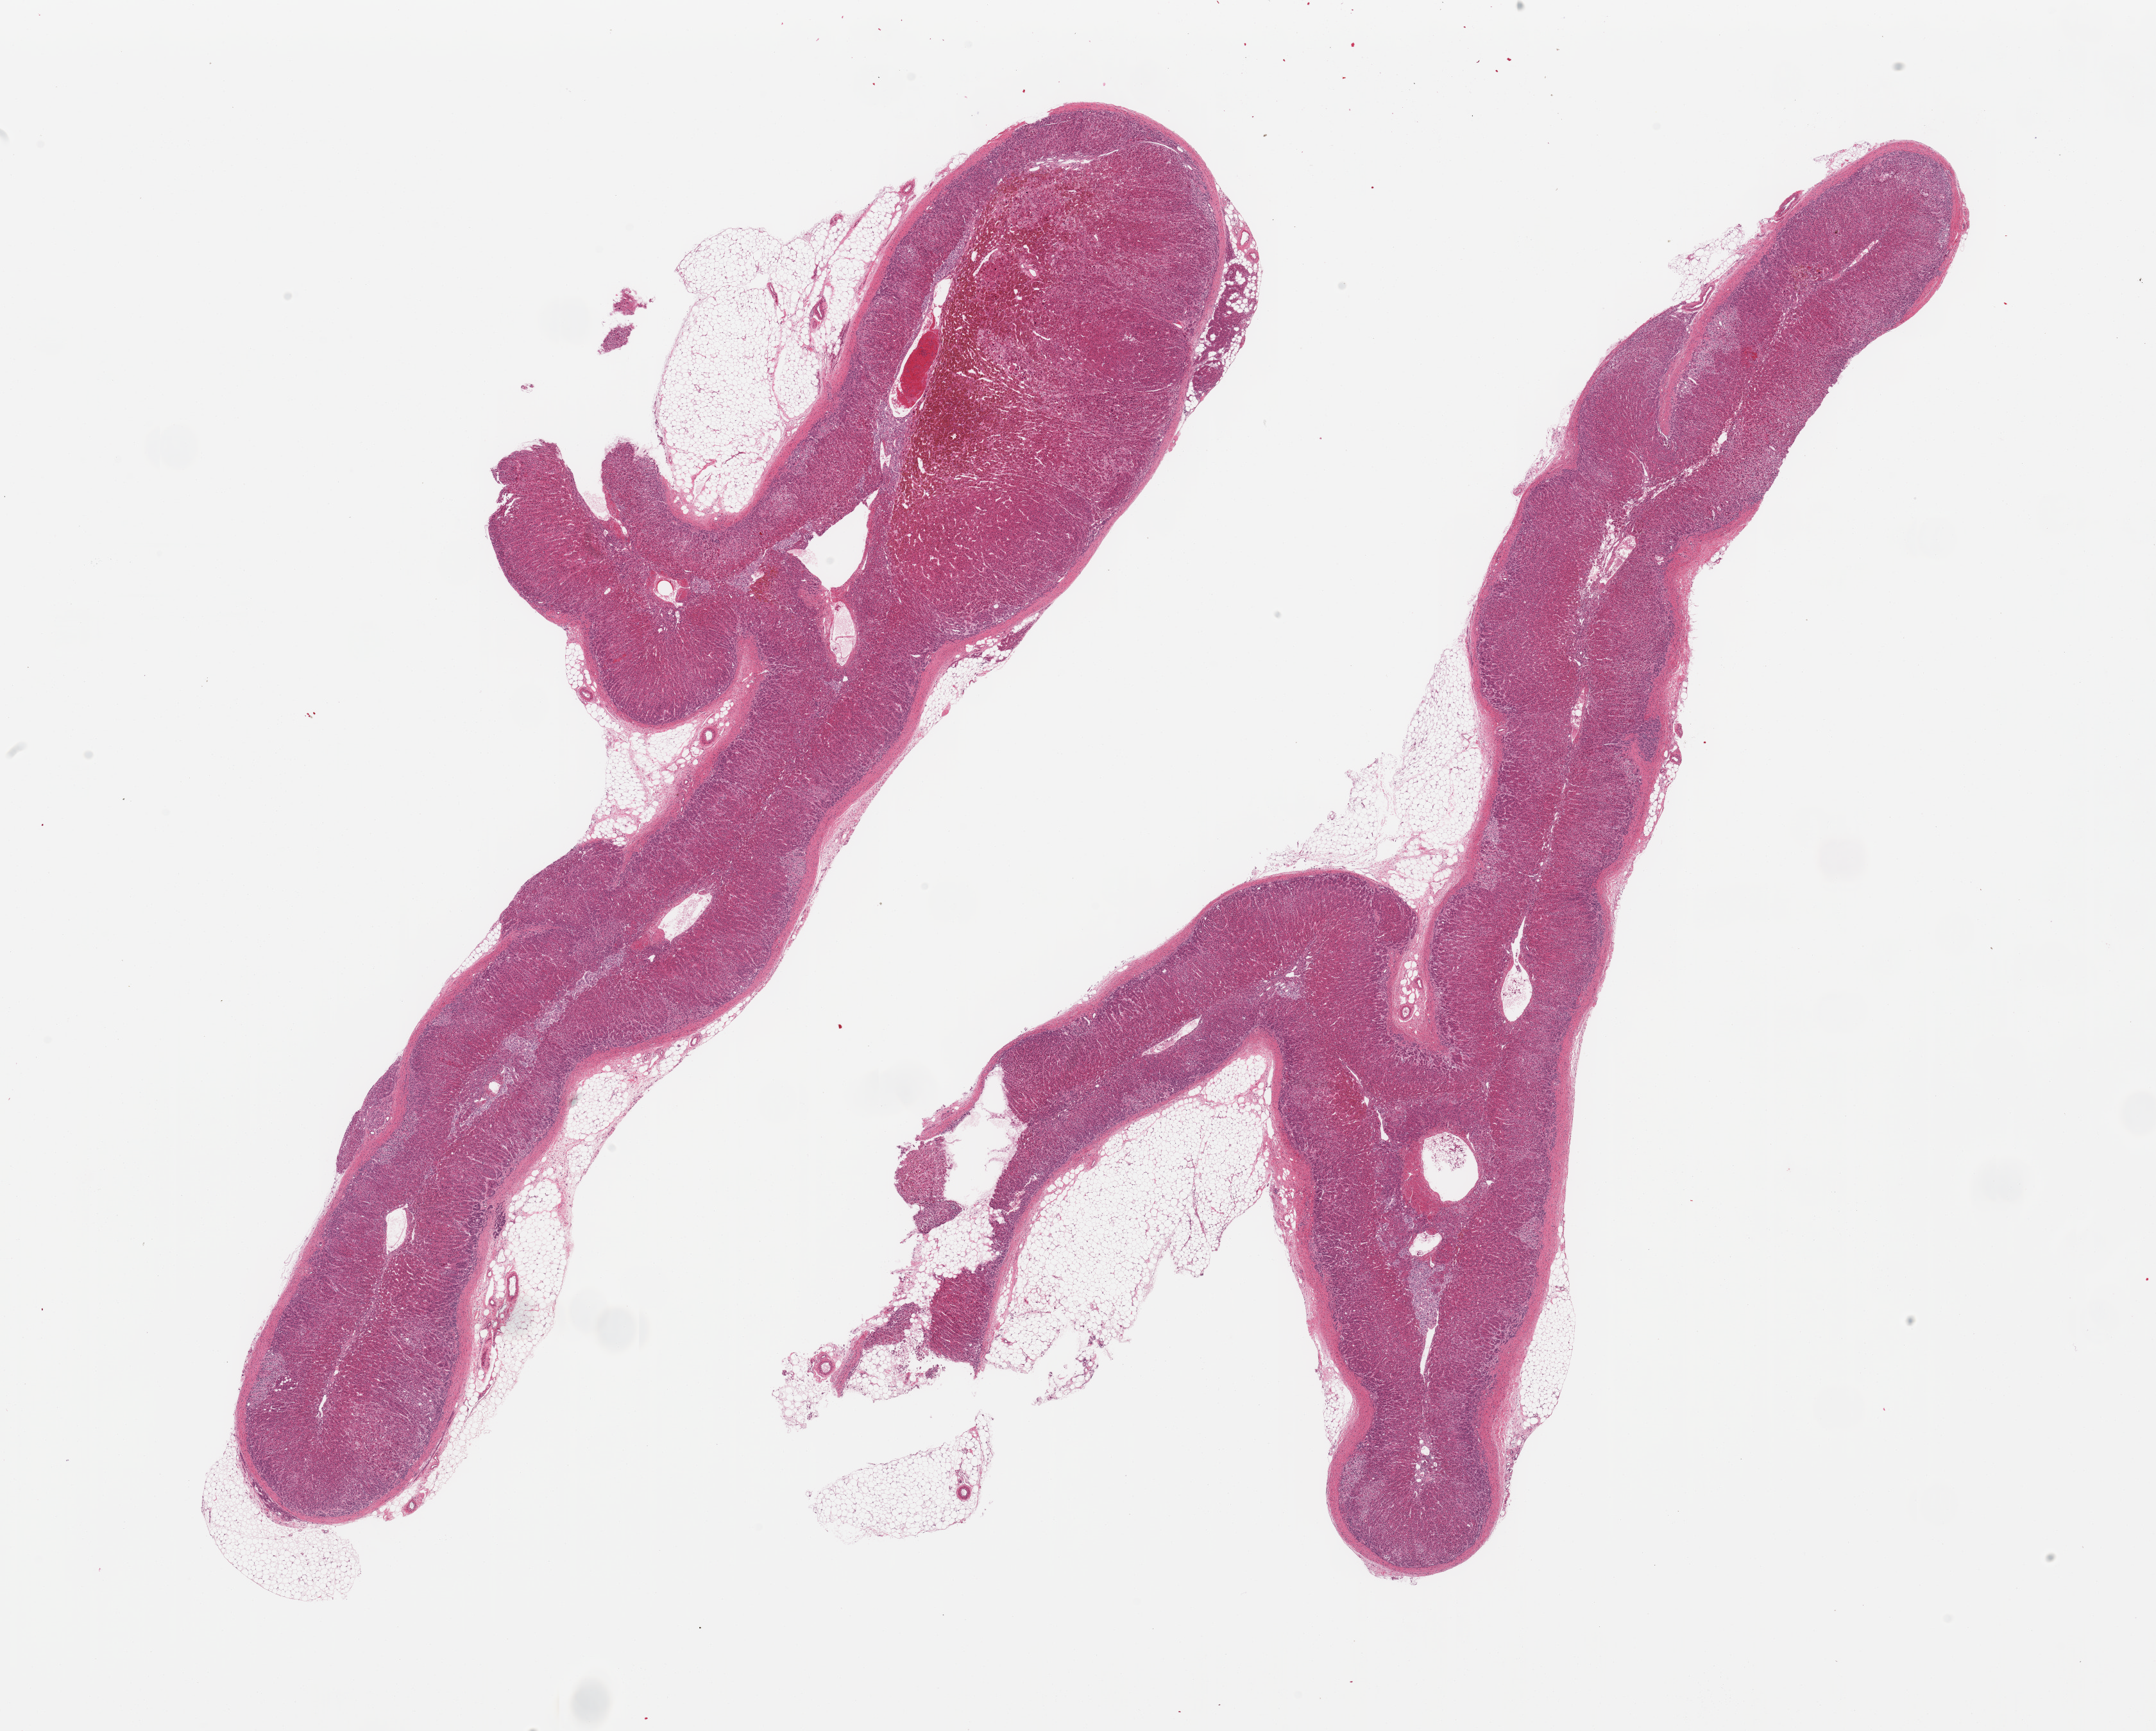
Whole-slide image, H&E stain, a low-resolution overview of the entire scanned area, about 26.6 x 21.3 mm (slide scanned at 20x). PAXgene-fixed paraffin-embedded (PFPE) section. Target tissue: adrenal gland. Donor tissue sample.
Review note (as recorded): 2 pieces; include 10-20% attached fat, cortex and medulla.